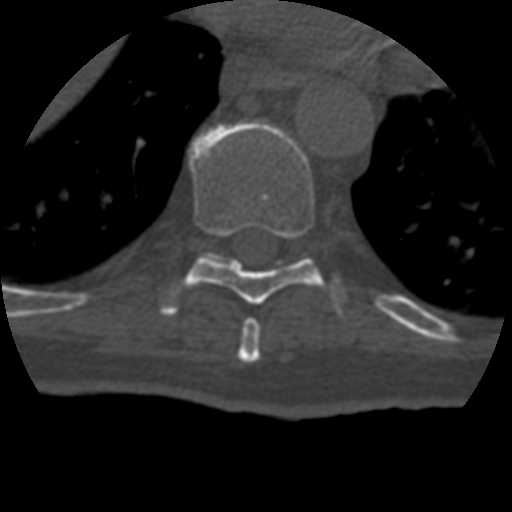
CT including the spine, one axial slice. Slice 237 of 399 in the series (ordered by position). Reconstruction kernel STANDARD. Bone window (W 1800 / L 400 HU). 1.25 mm slice thickness. 512 × 512 image matrix, field of view 160 × 160 mm. Patient age 69 years. From the clinical record (not read from this slice): primary cancer: prostate.
Annotated regions visible in this slice (semi-automatic segmentation, software-assisted and operator-edited):
- T10 vertebra: box from (x=206, y=252) to (x=219, y=261) px
- T8 vertebra: (x=237, y=318)–(x=261, y=363)
- T9 vertebra: (x=161, y=121)–(x=341, y=316)